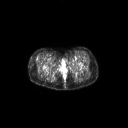
FDG PET of an extremity soft-tissue mass (from a PET/CT study), one axial slice; slice 48 of 267 in the series (ordered by position); 3.27 mm slice thickness; 128 × 128 image matrix, field of view 700 × 700 mm. Female patient, age 34 years. Case-level facts recorded for this patient, not image findings: histological type: synovial sarcoma; grade: intermediate; site of the primary tumour: right thigh.
Structures marked on this image (expert contour drawn on MRI and transferred to this co-registered scan by the dataset authors):
- gross tumour volume including surrounding oedema: bounding box [x1, y1, x2, y2] px = [35, 58, 37, 61]
- gross tumour volume (mass): [35, 58, 37, 61]